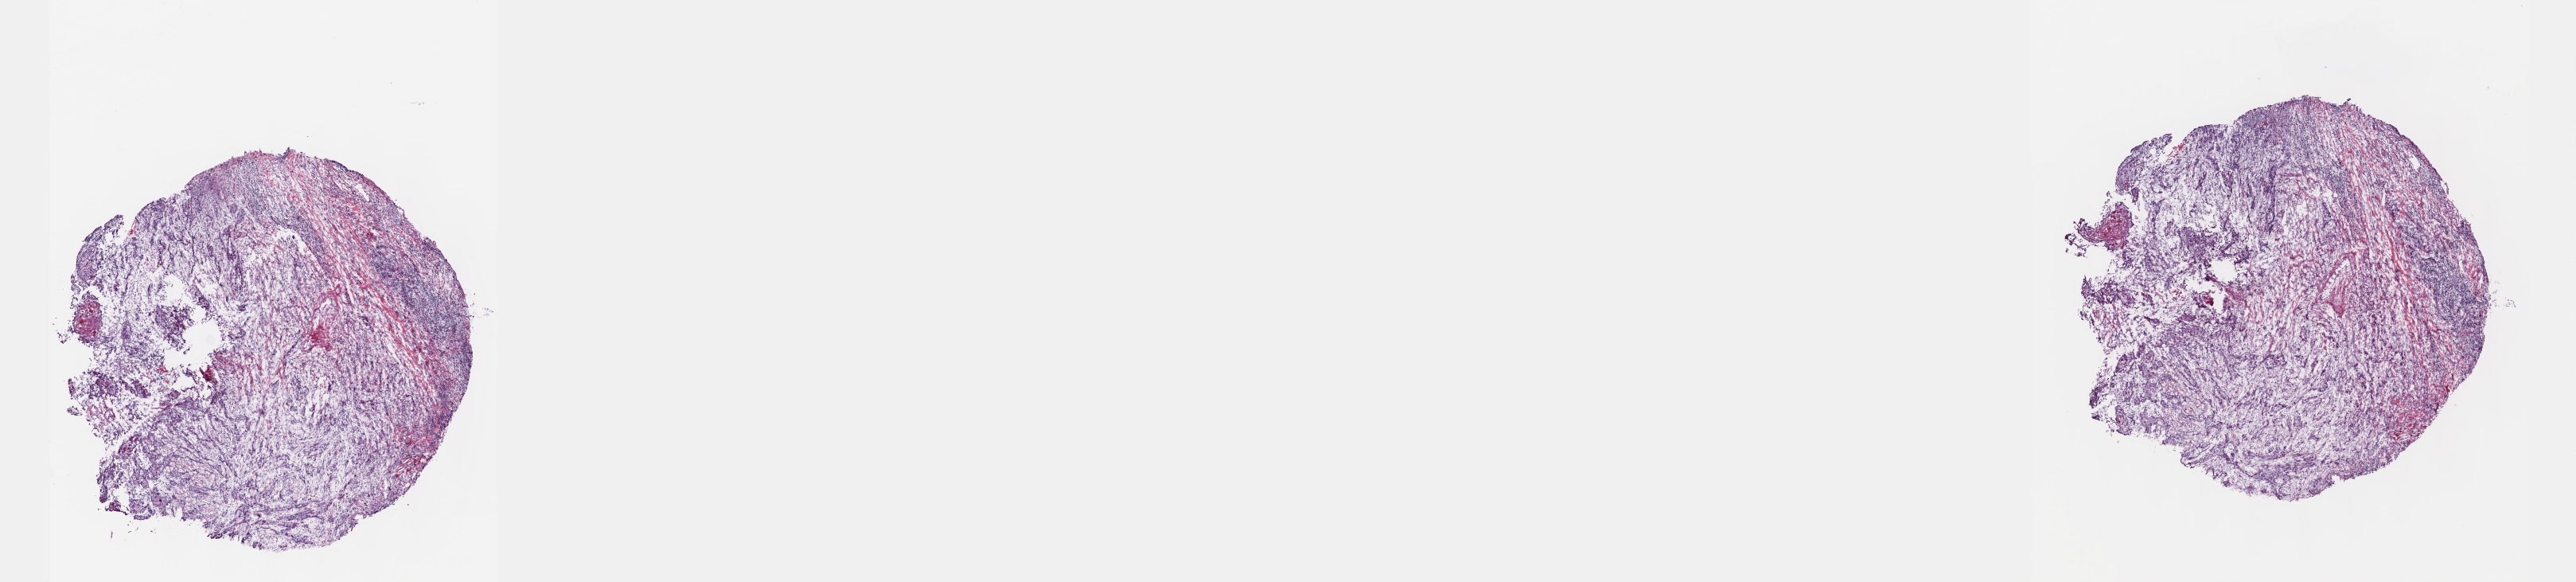
Whole-slide histology image, H&E-stained — whole scanned area (about 26.2 x 5.9 mm) shown as a low-resolution overview. Frozen section. Primary tumour sample from the head and neck. Patient: male, age at initial diagnosis 69 years. Histologic grade: G3 (poorly differentiated). Pathologist review of this section (percent, as recorded): tumour cells 60%, tumour nuclei 60%, normal cells 0%, stromal cells 40%, necrosis 0%. Infiltration values recorded for this section: lymphocyte infiltration 60%, monocyte infiltration 10%, neutrophil infiltration 20%.
AJCC pathologic stage: II. TNM: T2 N0. Pathologic diagnosis: Squamous cell carcinoma, keratinizing, NOS (tongue, NOS).